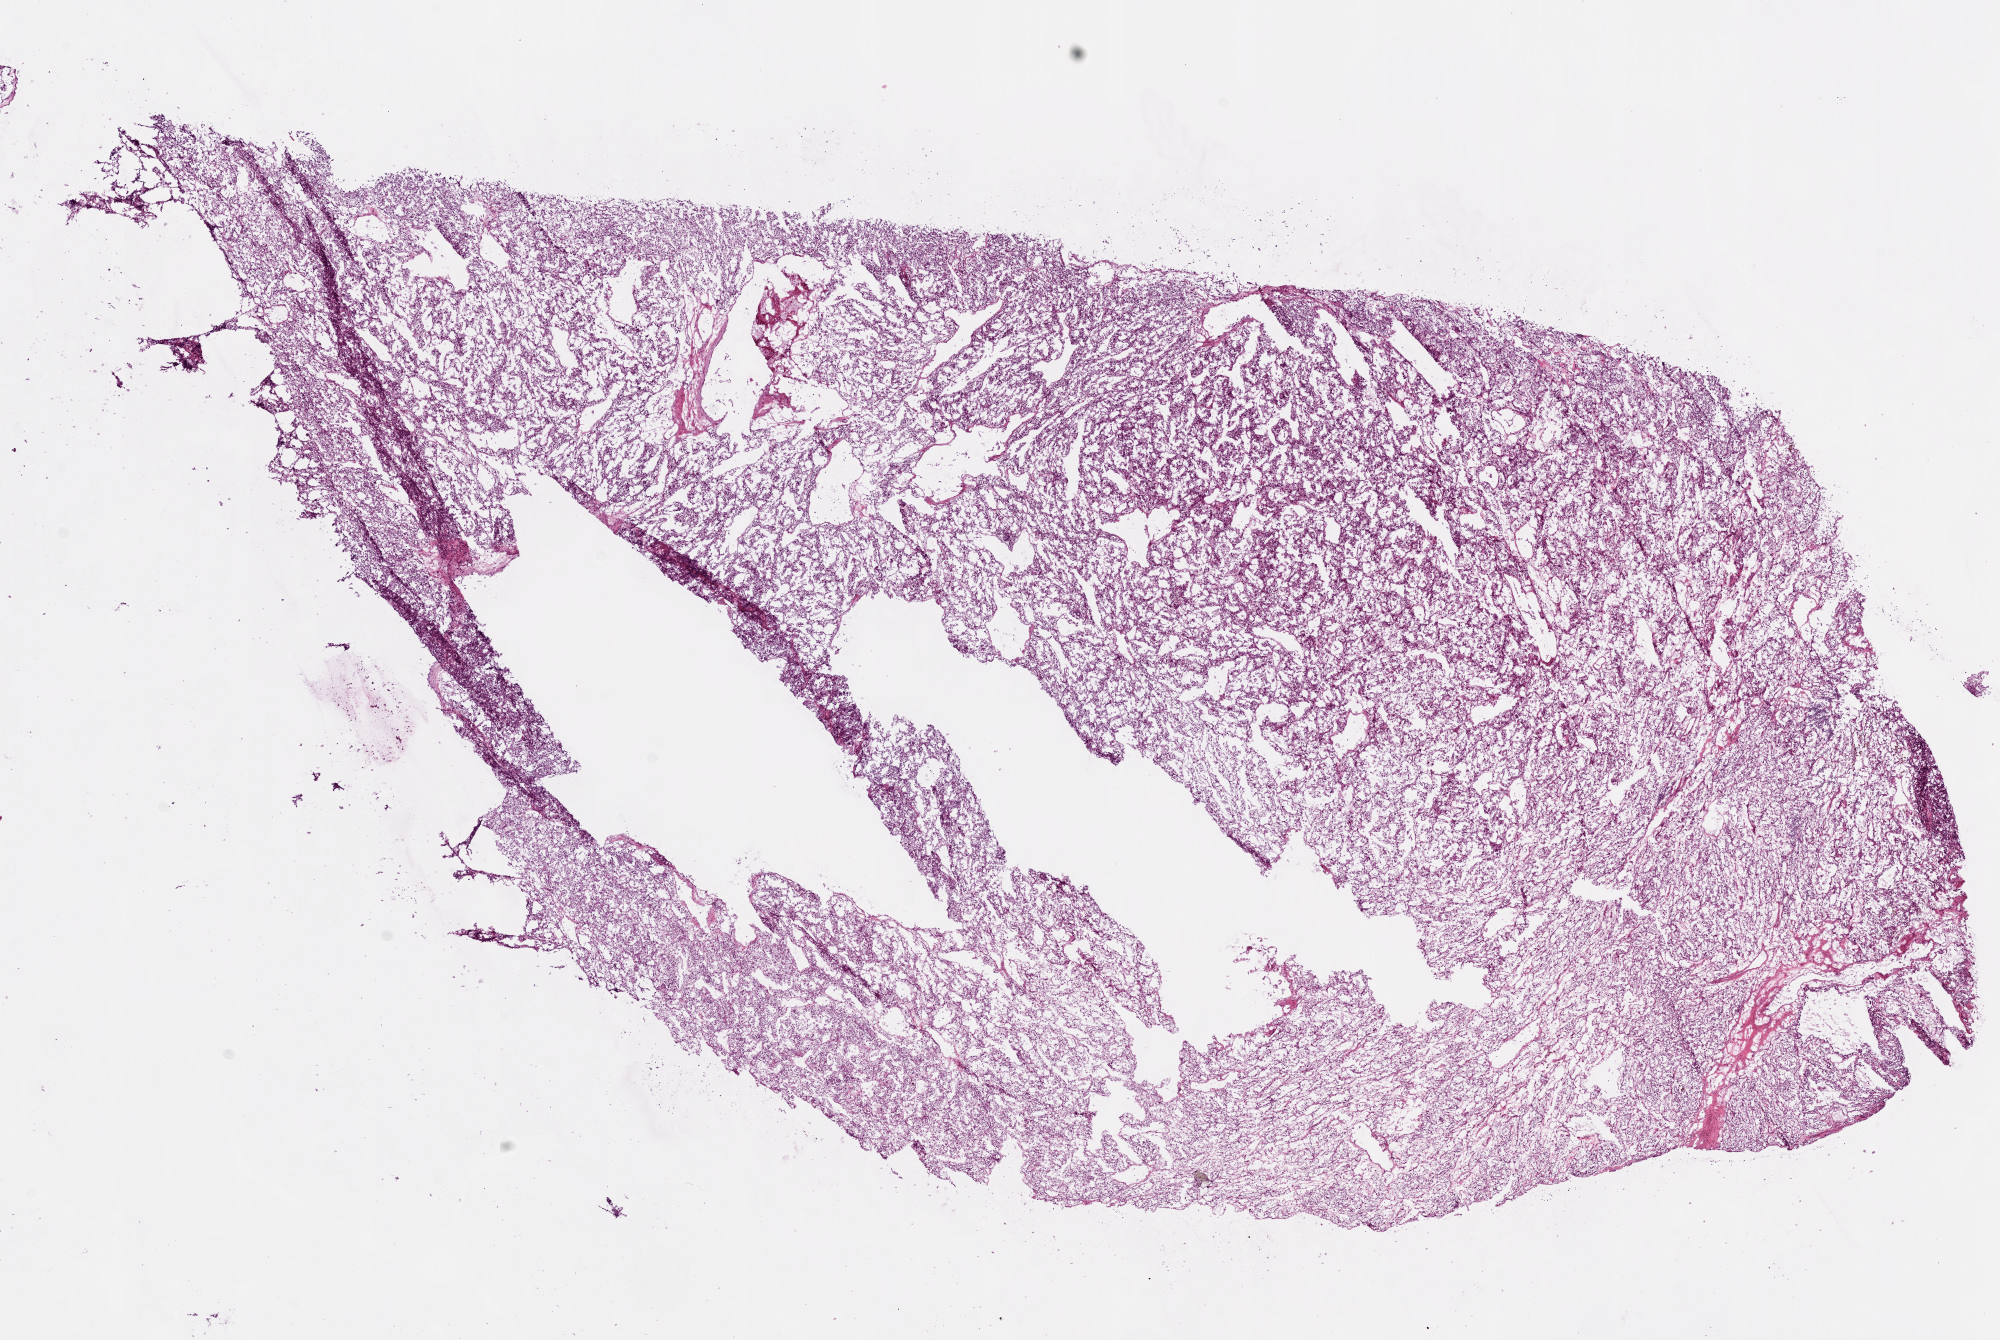
Digitized H&E tissue section (whole slide), whole scanned area (about 16.0 x 10.8 mm, slide scanned at 20x) shown as a low-resolution overview. Frozen section from the top of the tissue portion. Sample: primary tumour, kidney. Patient: male, age at initial diagnosis 73 years. Histologic grade: G3 (poorly differentiated). Pathologist review of this section (percent, as recorded): tumour cells 92%, tumour nuclei 85%, normal cells 0%, stromal cells 8%, necrosis 0%.
AJCC pathologic stage: I (6th edition). Diagnosis: Clear cell adenocarcinoma, NOS.